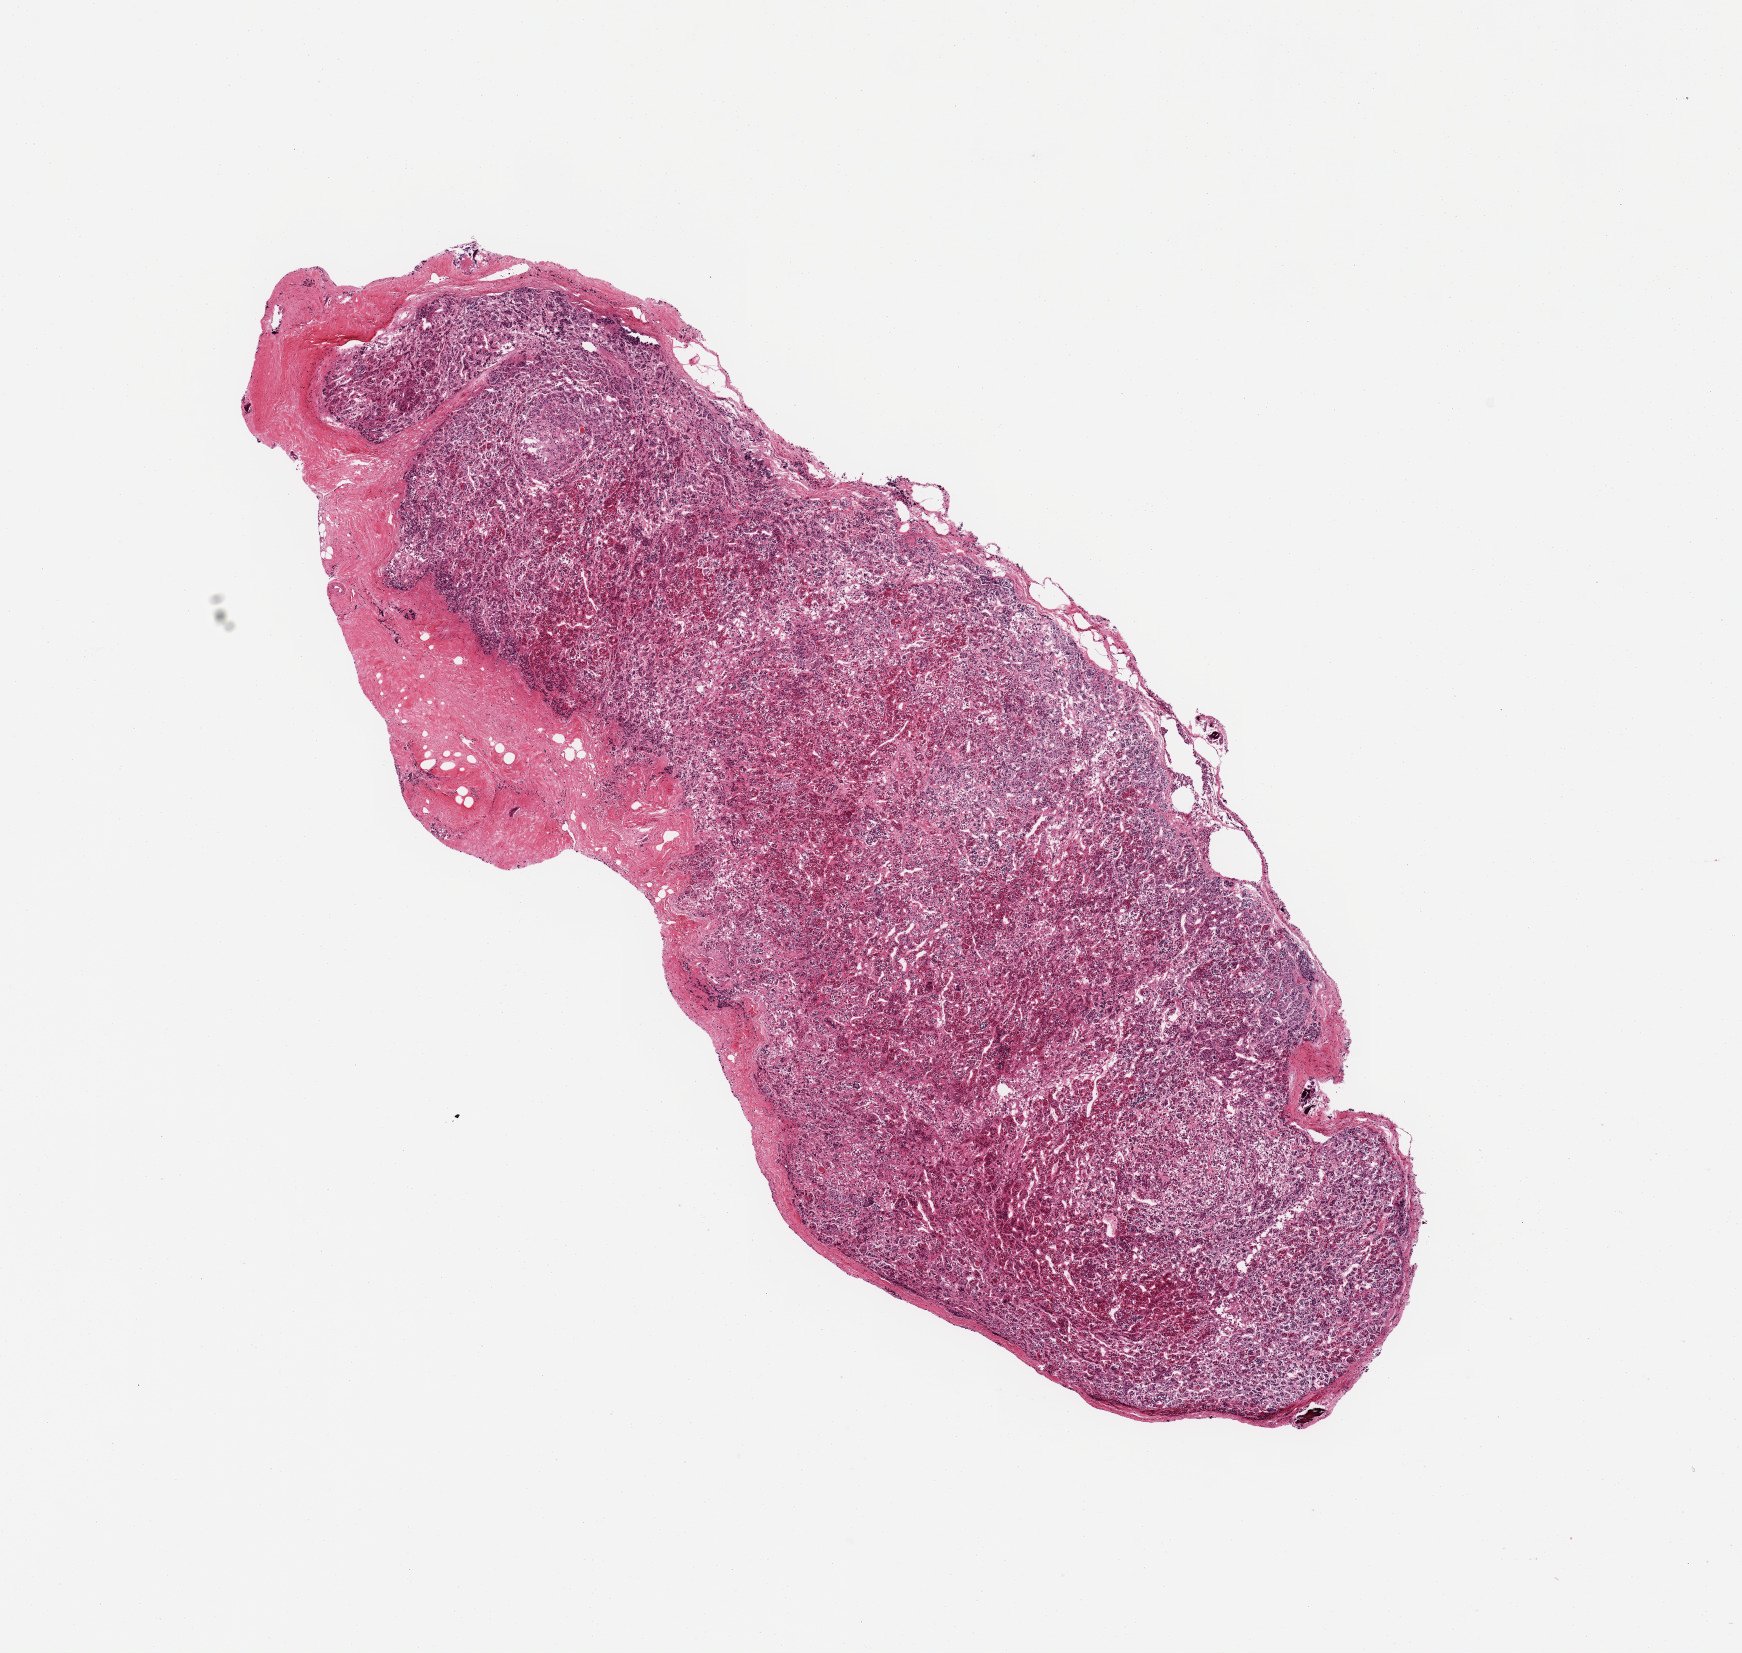
Digitized hematoxylin and eosin (H&E)-stained section, brightfield — whole scanned area (about 13.8 x 13.1 mm) shown as a low-resolution overview; PAXgene-fixed, paraffin-embedded tissue; section of pituitary (target tissue); donor tissue sample. Male donor.
Reviewer comment on this tissue sample: 1 piece; adenohypophysis, ~adherent dura focally up to ~1mm.